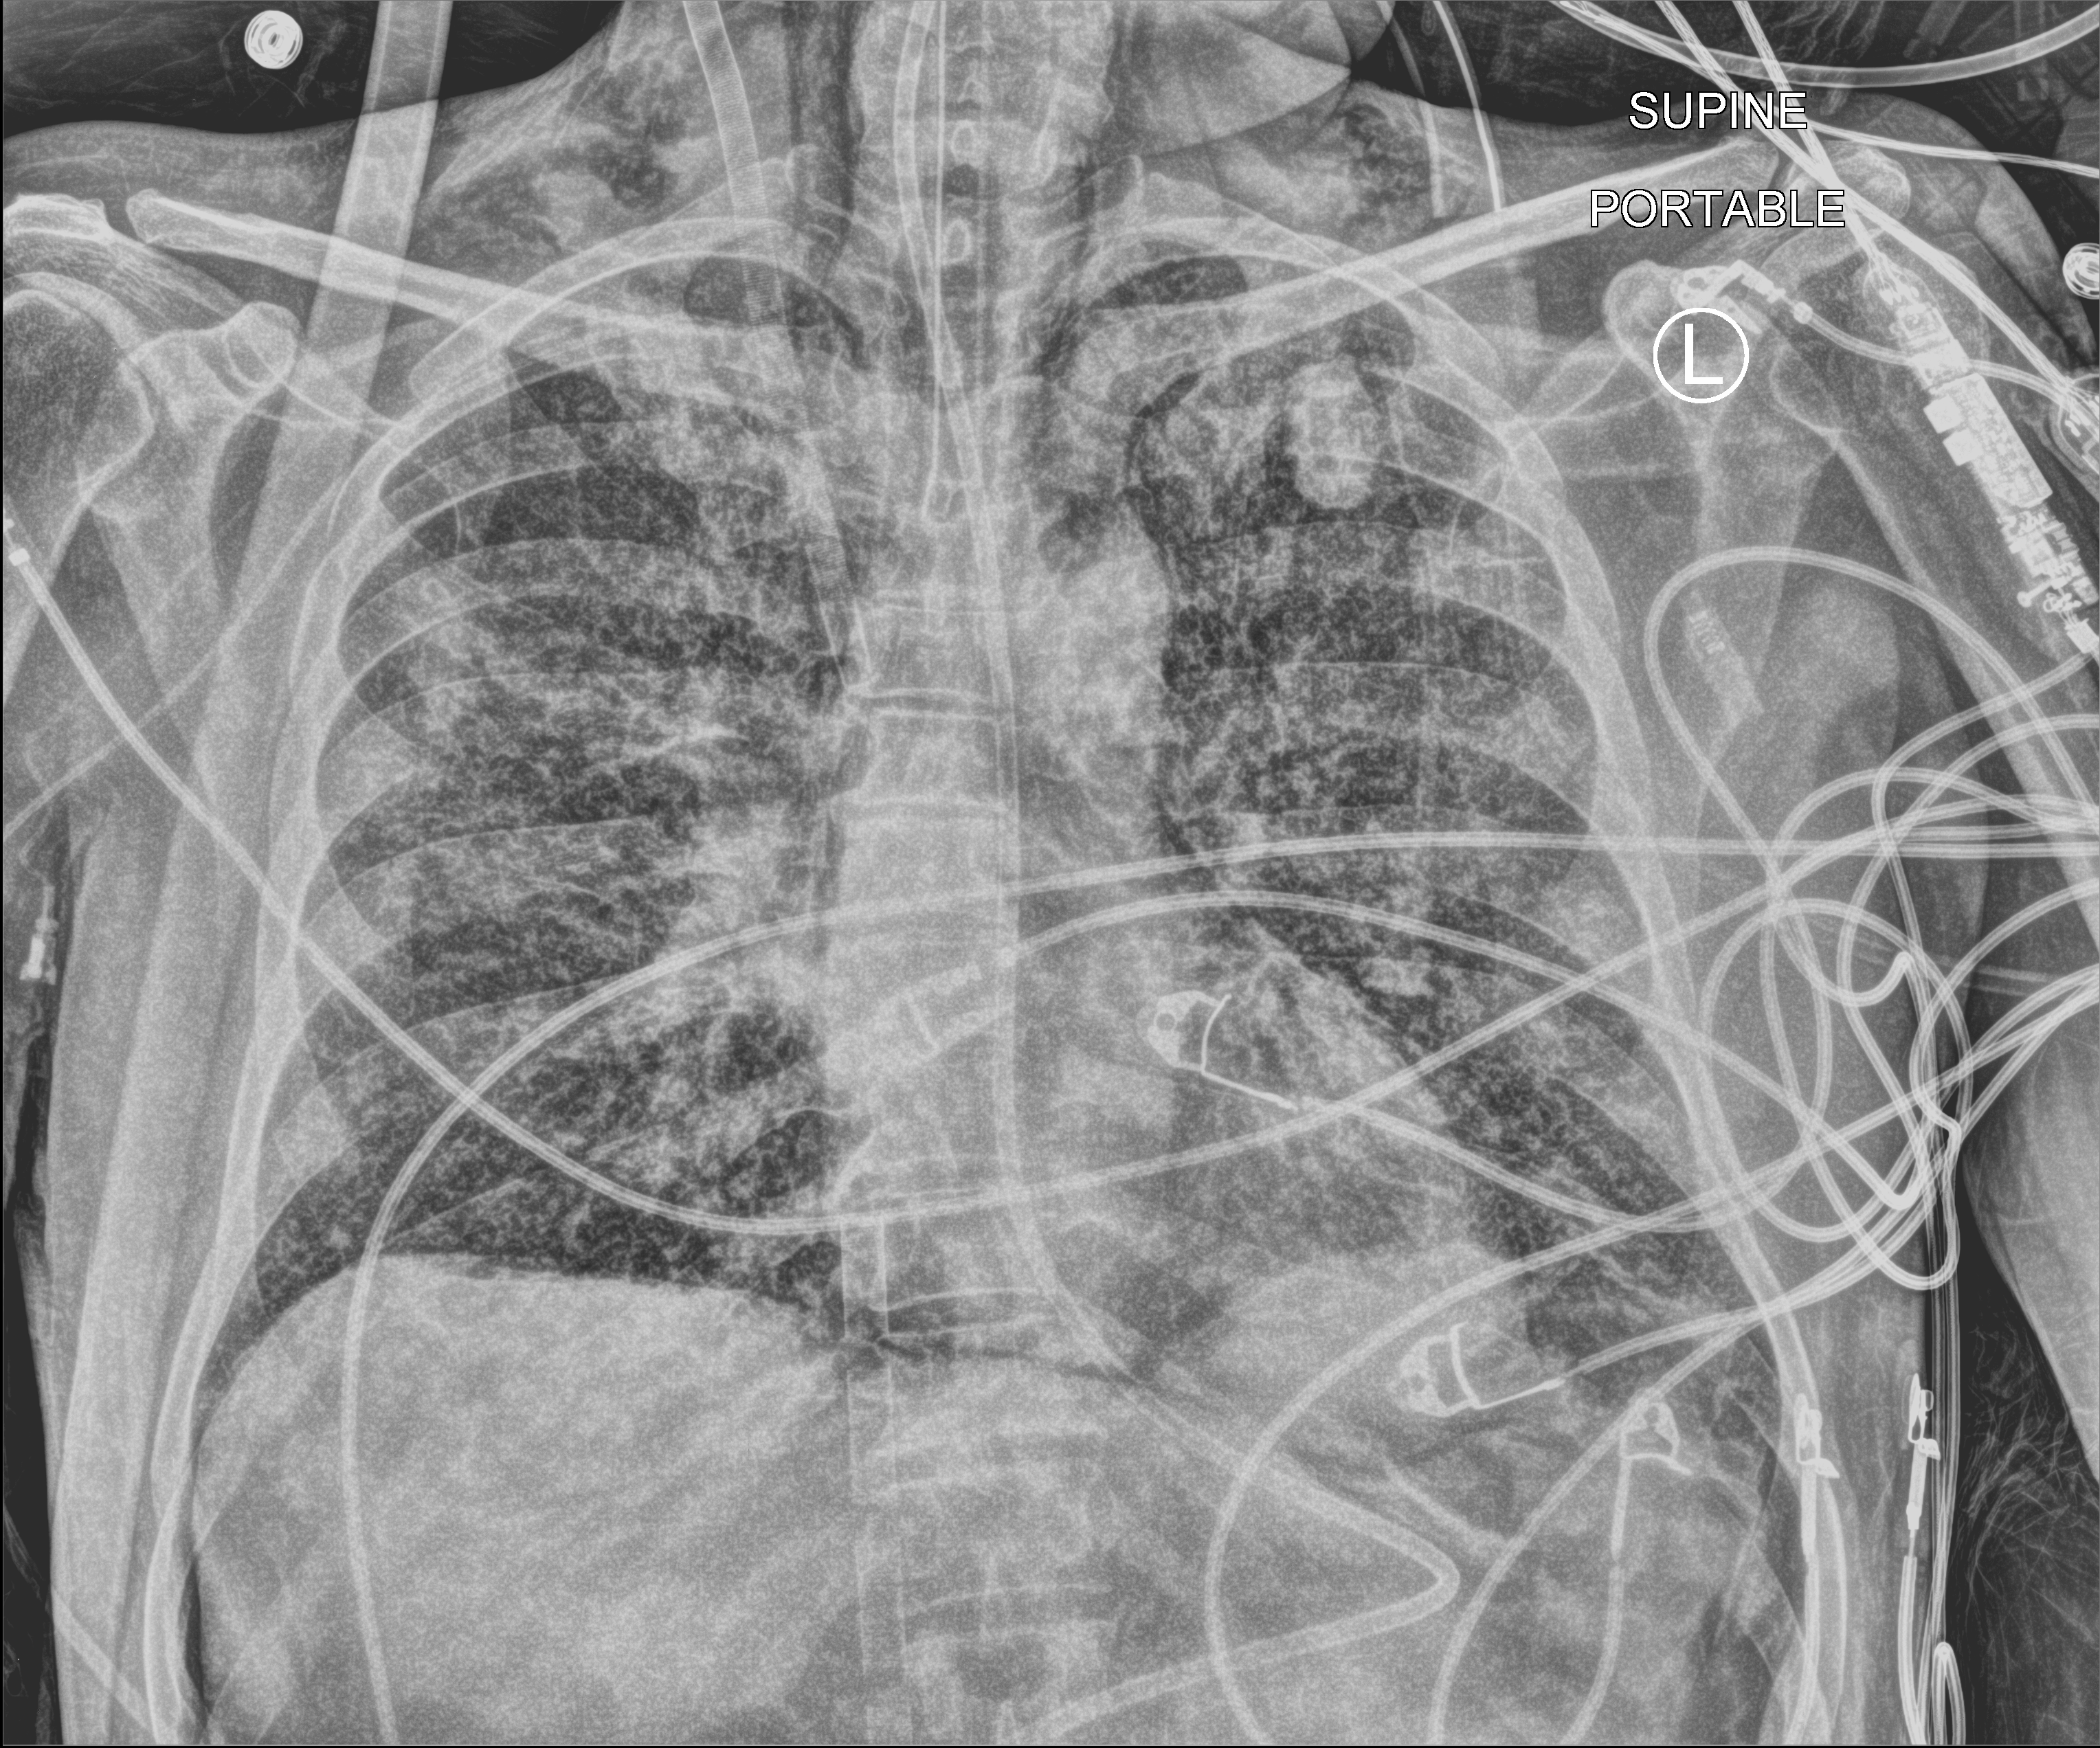
Chest X-ray (portable), anteroposterior (AP) projection. Patient hospitalised with COVID-19; male, aged 18–59 years.
Hospital-stay facts (about this admission, not read from this image; timing relative to this image not recorded):
- diabetes (admission record): no
- other chronic lung disease (admission record): no
- admitted to intensive care during this hospital stay: yes